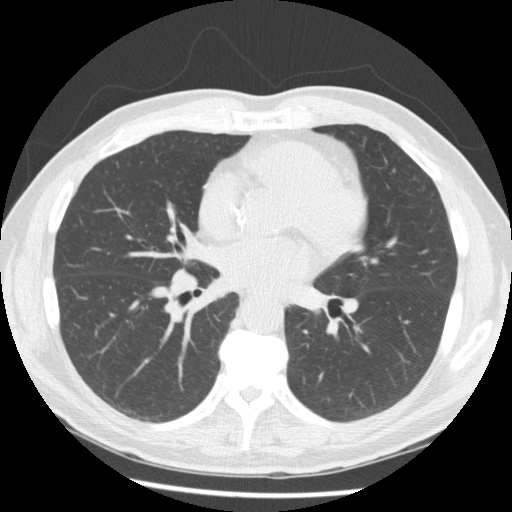
Axial slice from a low-dose chest CT screening exam, baseline screening round, lung window (W 1500 / L -600 HU), 2.5 mm slice thickness, standard (soft-tissue) reconstruction kernel (STANDARD), 512 × 512 image matrix. Male participant, aged 62 years at enrolment. Current smoker at enrolment.
• Lesion marked by an expert reader, box from (x=153, y=253) to (x=215, y=310) px.
• Screening reader's record for this exam: no non-calcified nodule ≥4 mm recorded.
• Official screen result: negative screen, minor abnormalities not suspicious for lung cancer.
• Lung cancer was diagnosed 146 days after this screen: small cell carcinoma, NOS, right hilum, mediastinum, poorly differentiated (G3), stage IV (AJCC 6th edition).